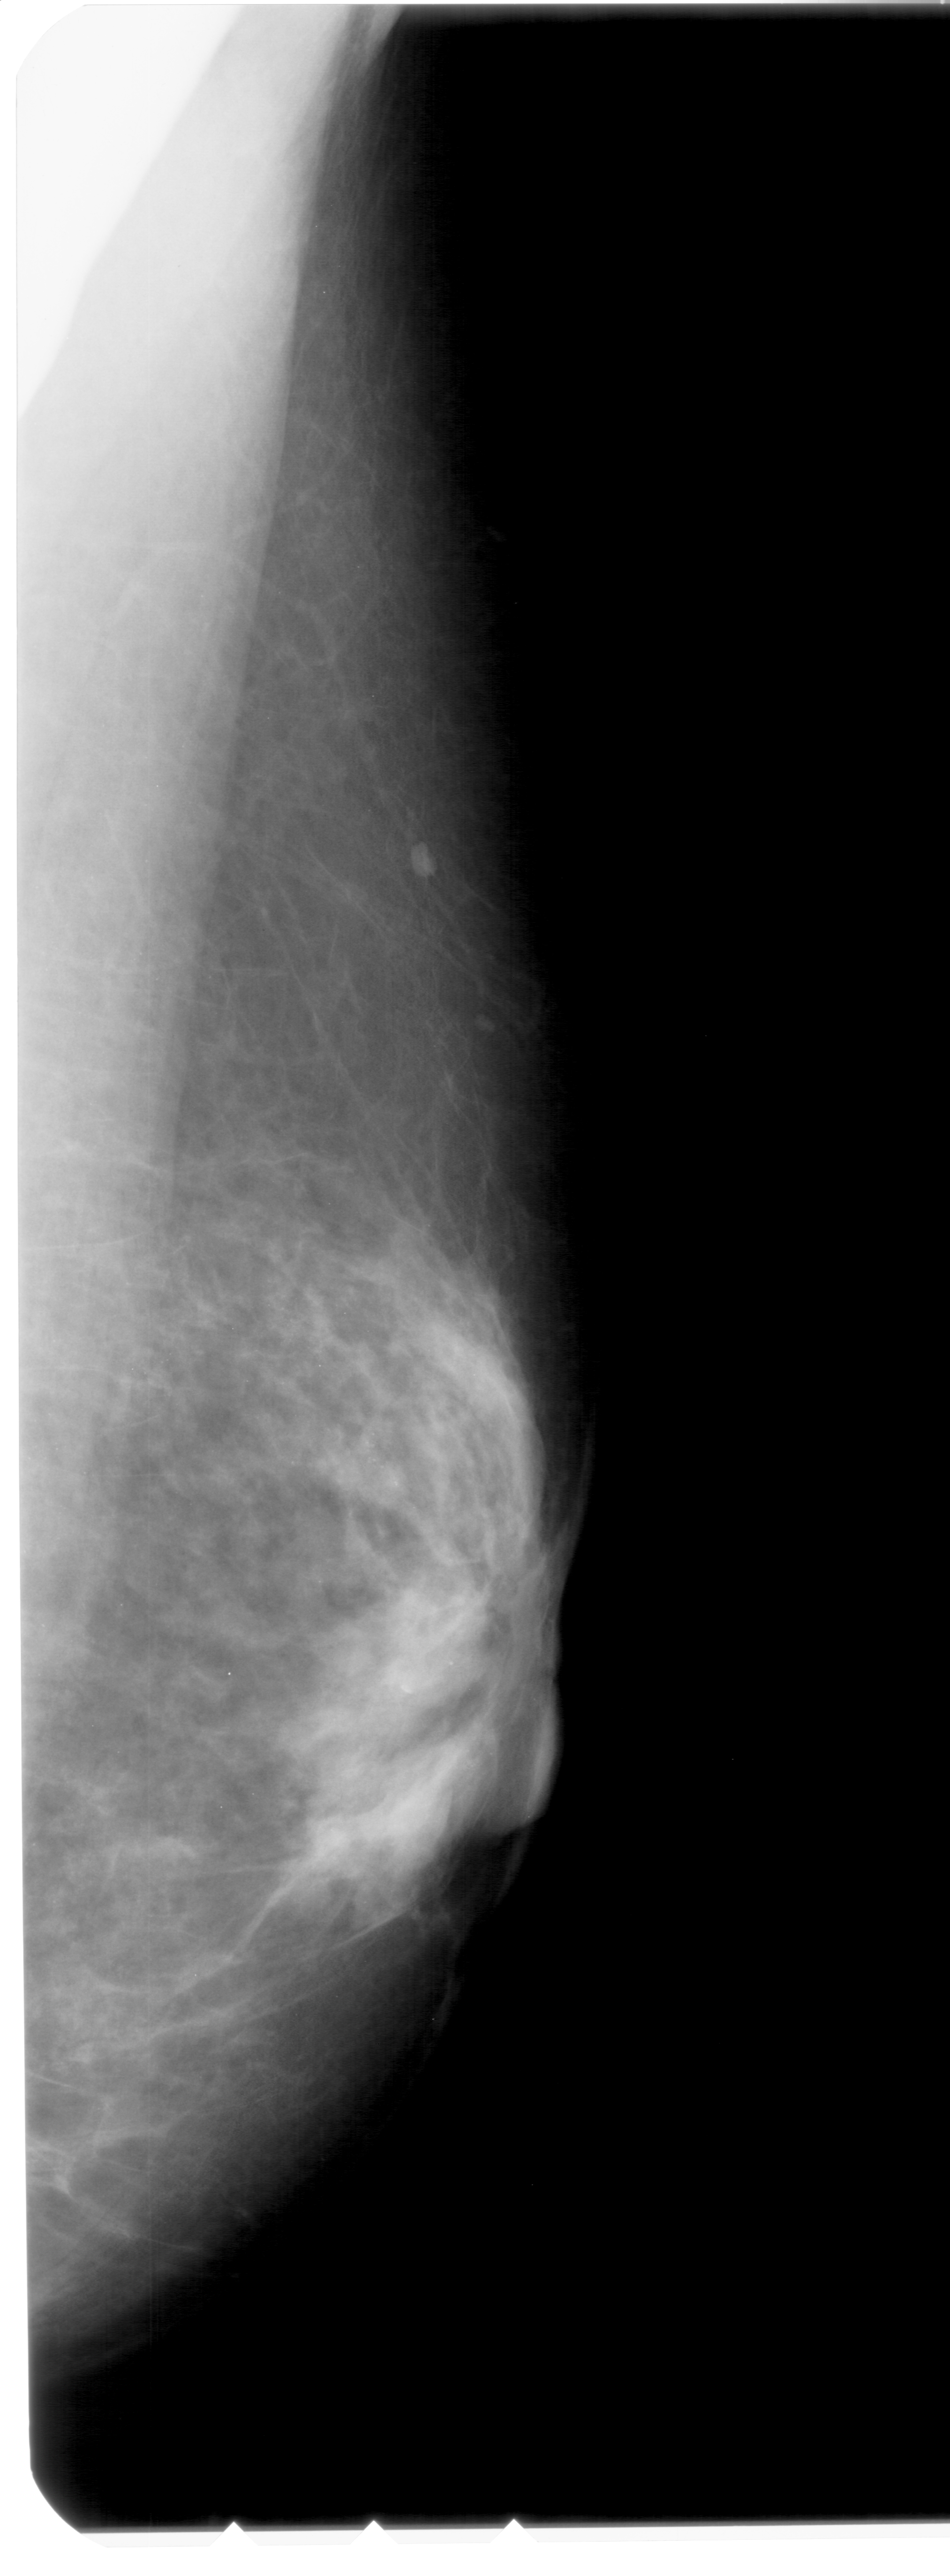
Mammogram (digitized film); right breast; mediolateral oblique (MLO) view; BI-RADS breast density category 3 (scale 1–4); 950 × 2576 image matrix.
Expert-marked regions of interest on this image (one box per marked abnormality):
- calcifications, morphology pleomorphic, distribution clustered; BI-RADS assessment category 4; subtlety rating 2 on a 1 (subtle) to 5 (obvious) scale; pathology result (as recorded, not read from the image): malignant: bounding box <335,1416,412,1523> (left, top, right, bottom; pixels)